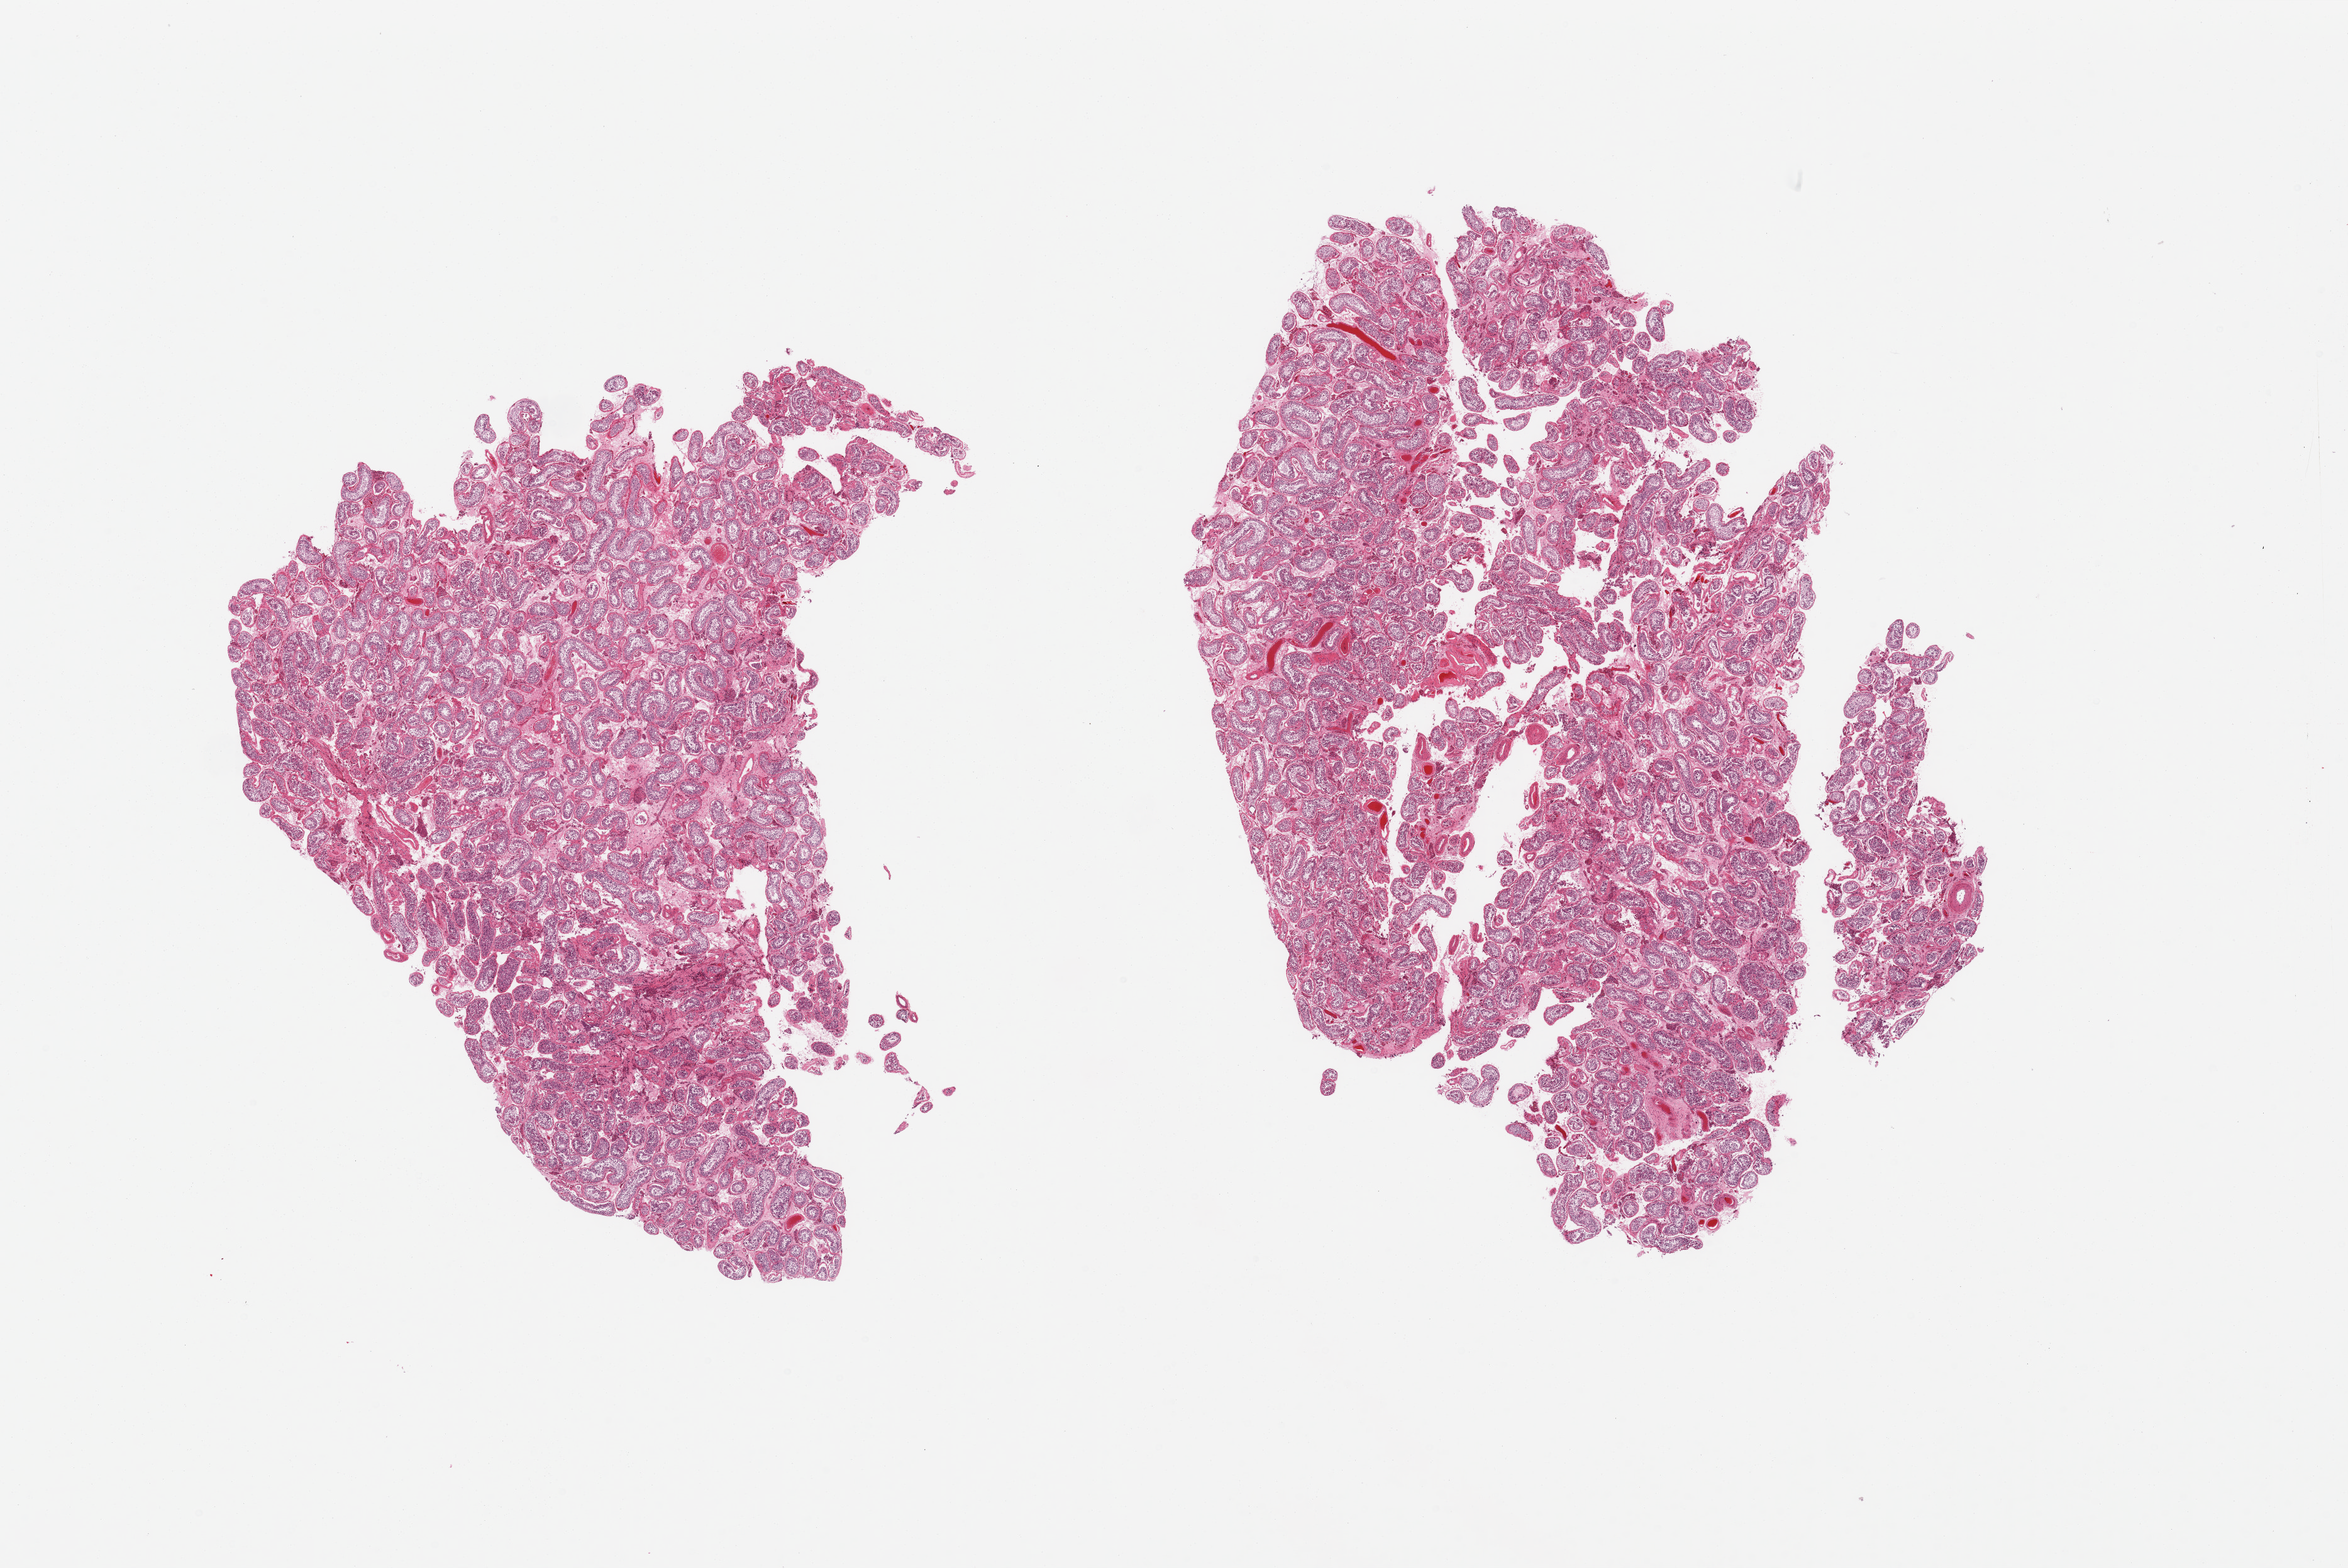
Haematoxylin and eosin whole-slide image, brightfield, whole scanned area (about 29.5 x 19.7 mm, from a 20x scan) shown as a low-resolution overview. PAXgene-fixed paraffin-embedded (PFPE) section. Section of testis (target tissue). Tissue donor sample.
Reviewer comment on this tissue sample: 2 pieces; spermatogenesis observed; congestion.